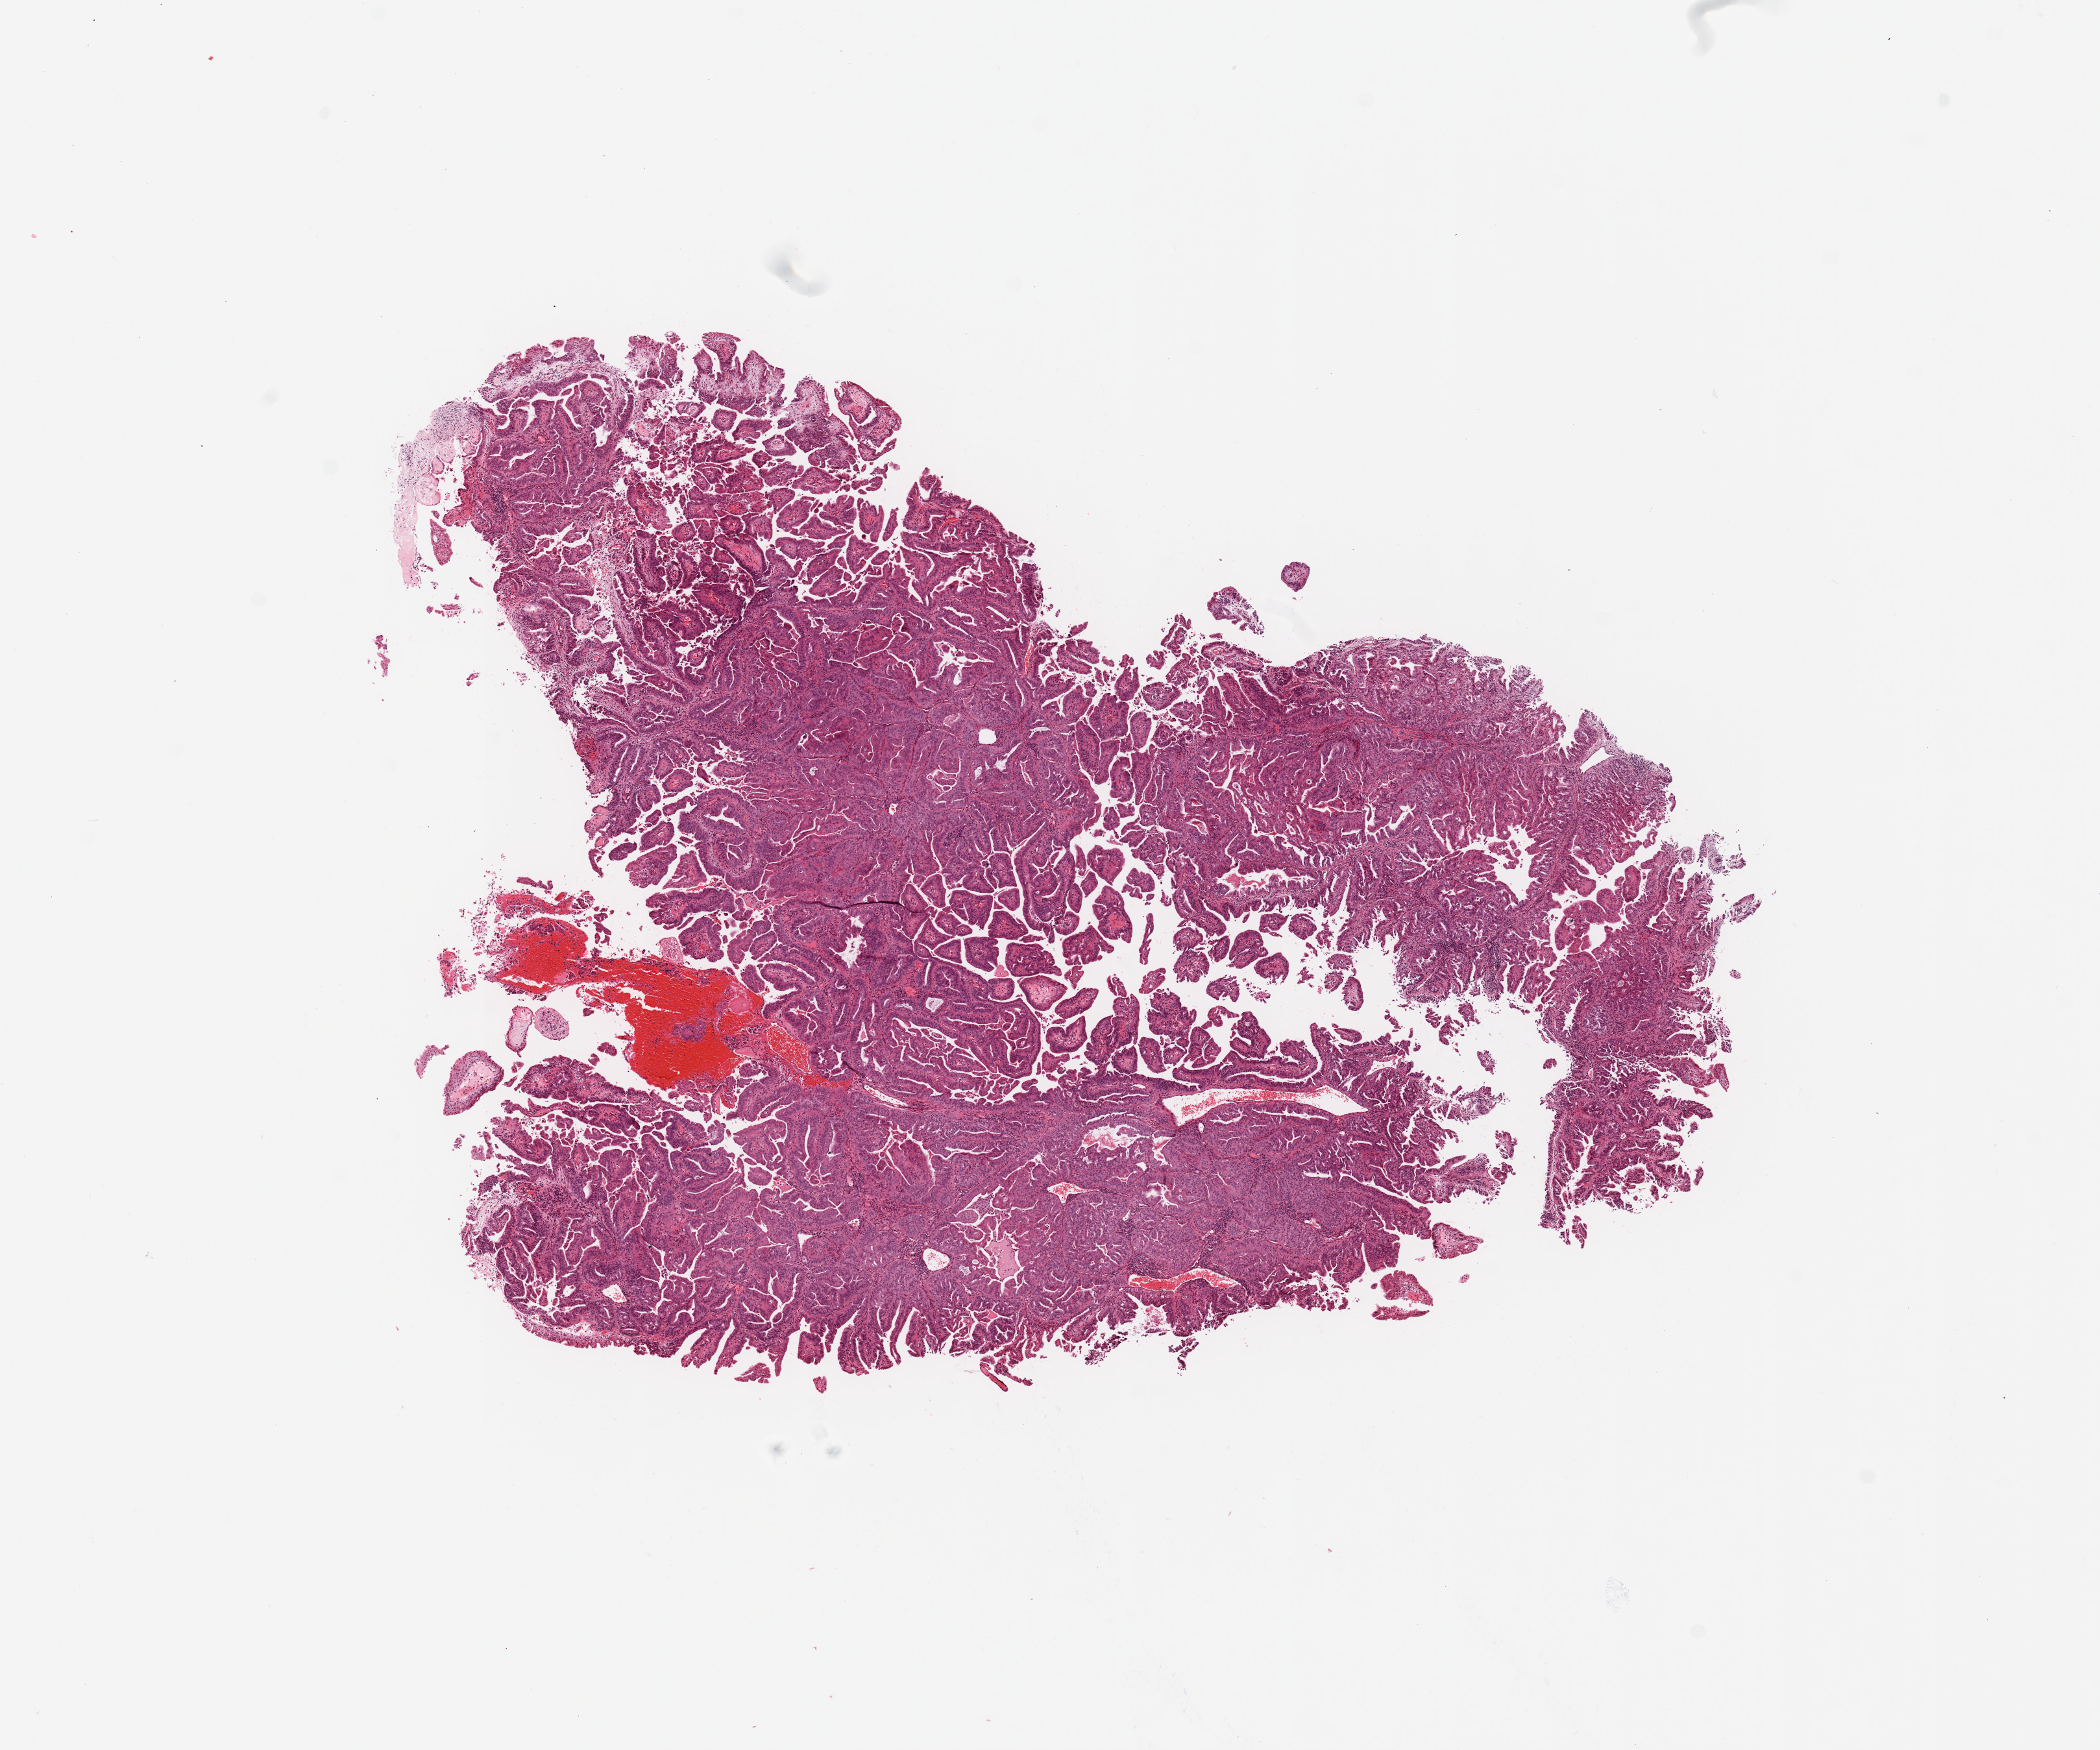
Whole-slide histology image, H&E-stained — low-resolution overview of the scanned area, about 12.8 x 10.7 mm; tumour tissue sample, uterus. Patient: female, age 66 years. Histologic grade: G2 (moderately differentiated).
Histologic diagnosis: Endometrioid adenocarcinoma, NOS. AJCC pathologic stage: IB.